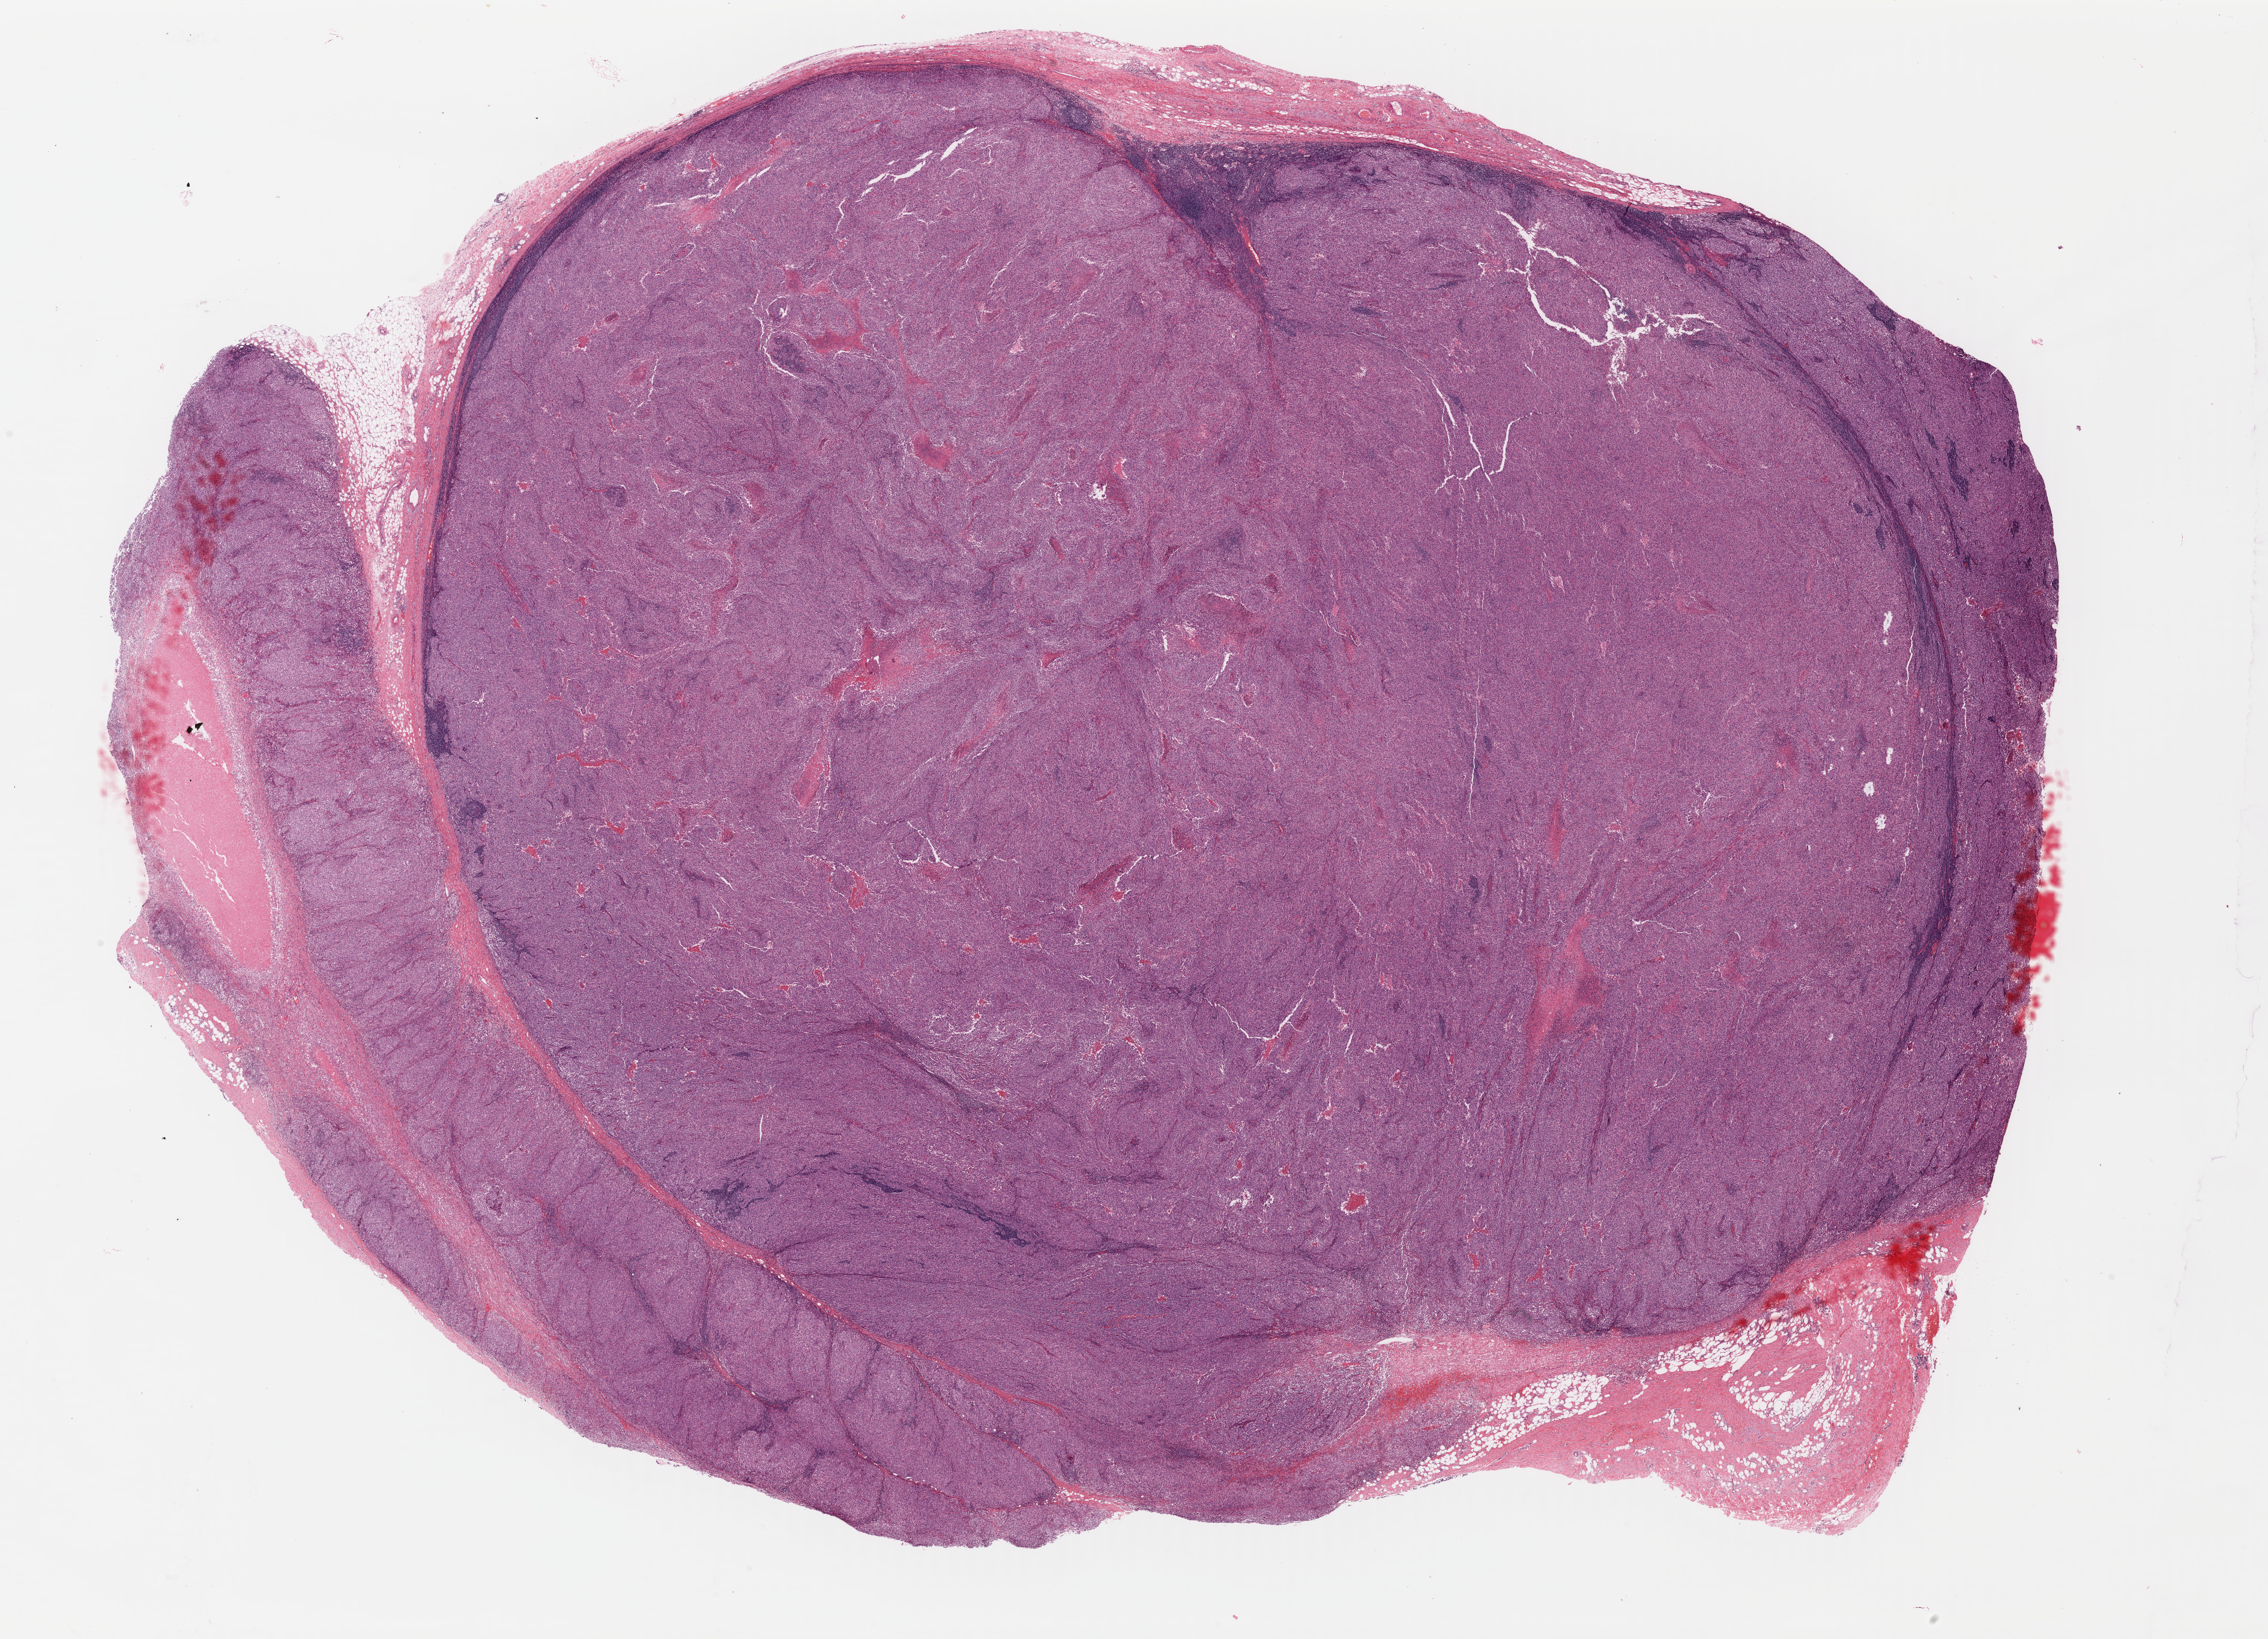
Digitized H&E tissue section (whole slide) — low-resolution overview of the scanned area, about 29.7 x 21.5 mm. Formalin-fixed paraffin-embedded (FFPE) diagnostic section. Primary tumour sample from the skin. Patient: female, age at initial diagnosis 51 years.
Diagnosis: Malignant melanoma, NOS.